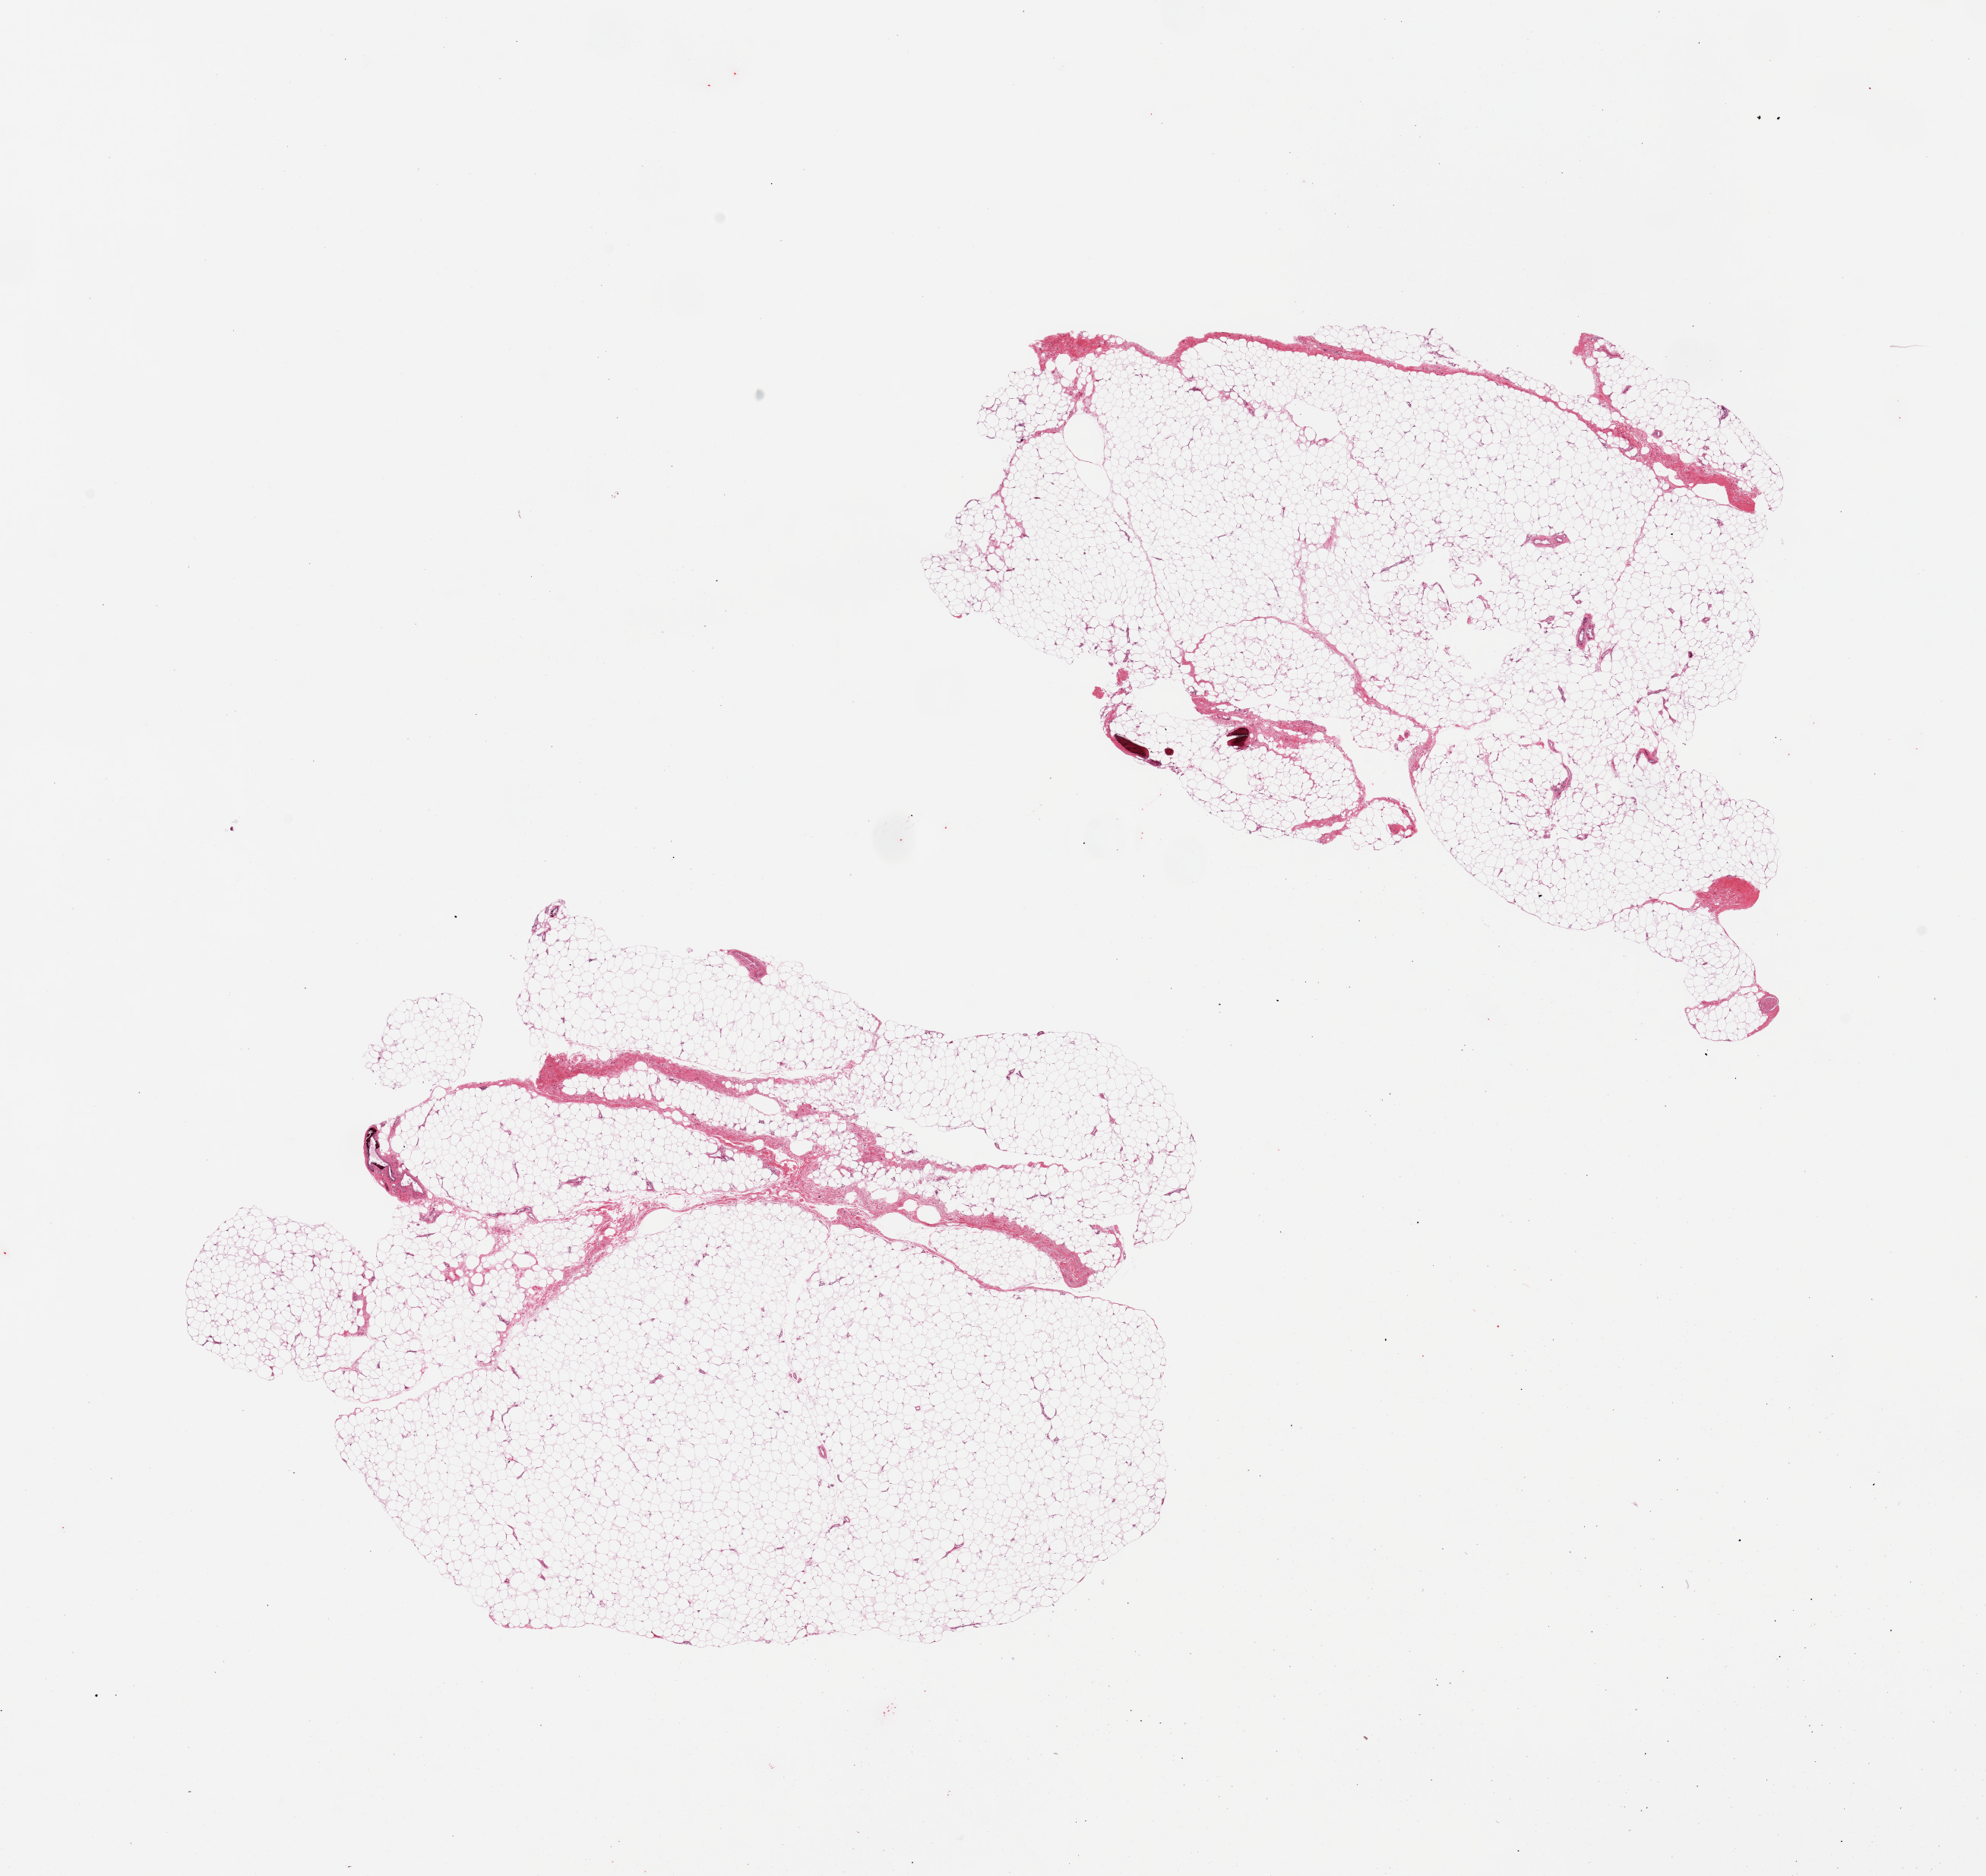
H&E whole-slide image, low-resolution overview of the scanned area, about 20.7 x 19.5 mm; PAXgene-fixed, paraffin-embedded tissue; sampled site (target tissue): adipose tissue; donor tissue sample. Donor sex: female.
Review note (as recorded): 2 pieces, focal vascular calicification.